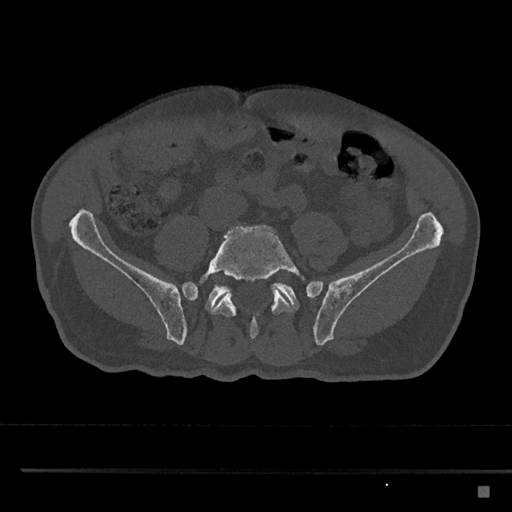
CT including the spine, one axial slice. Slice 570 of 797 in the series (ordered by position). 120 kVp. Bone window (W 1800 / L 400 HU). 0.5 mm slice thickness. 512 × 512 image matrix. Male patient, age 59 years. Case-level facts recorded for this patient, not image findings: primary cancer: prostate.
Outlined on this slice (semi-automatic segmentation, software-assisted and operator-edited):
- L5 vertebra: bounding box <199,225,305,339> (left, top, right, bottom; pixels)